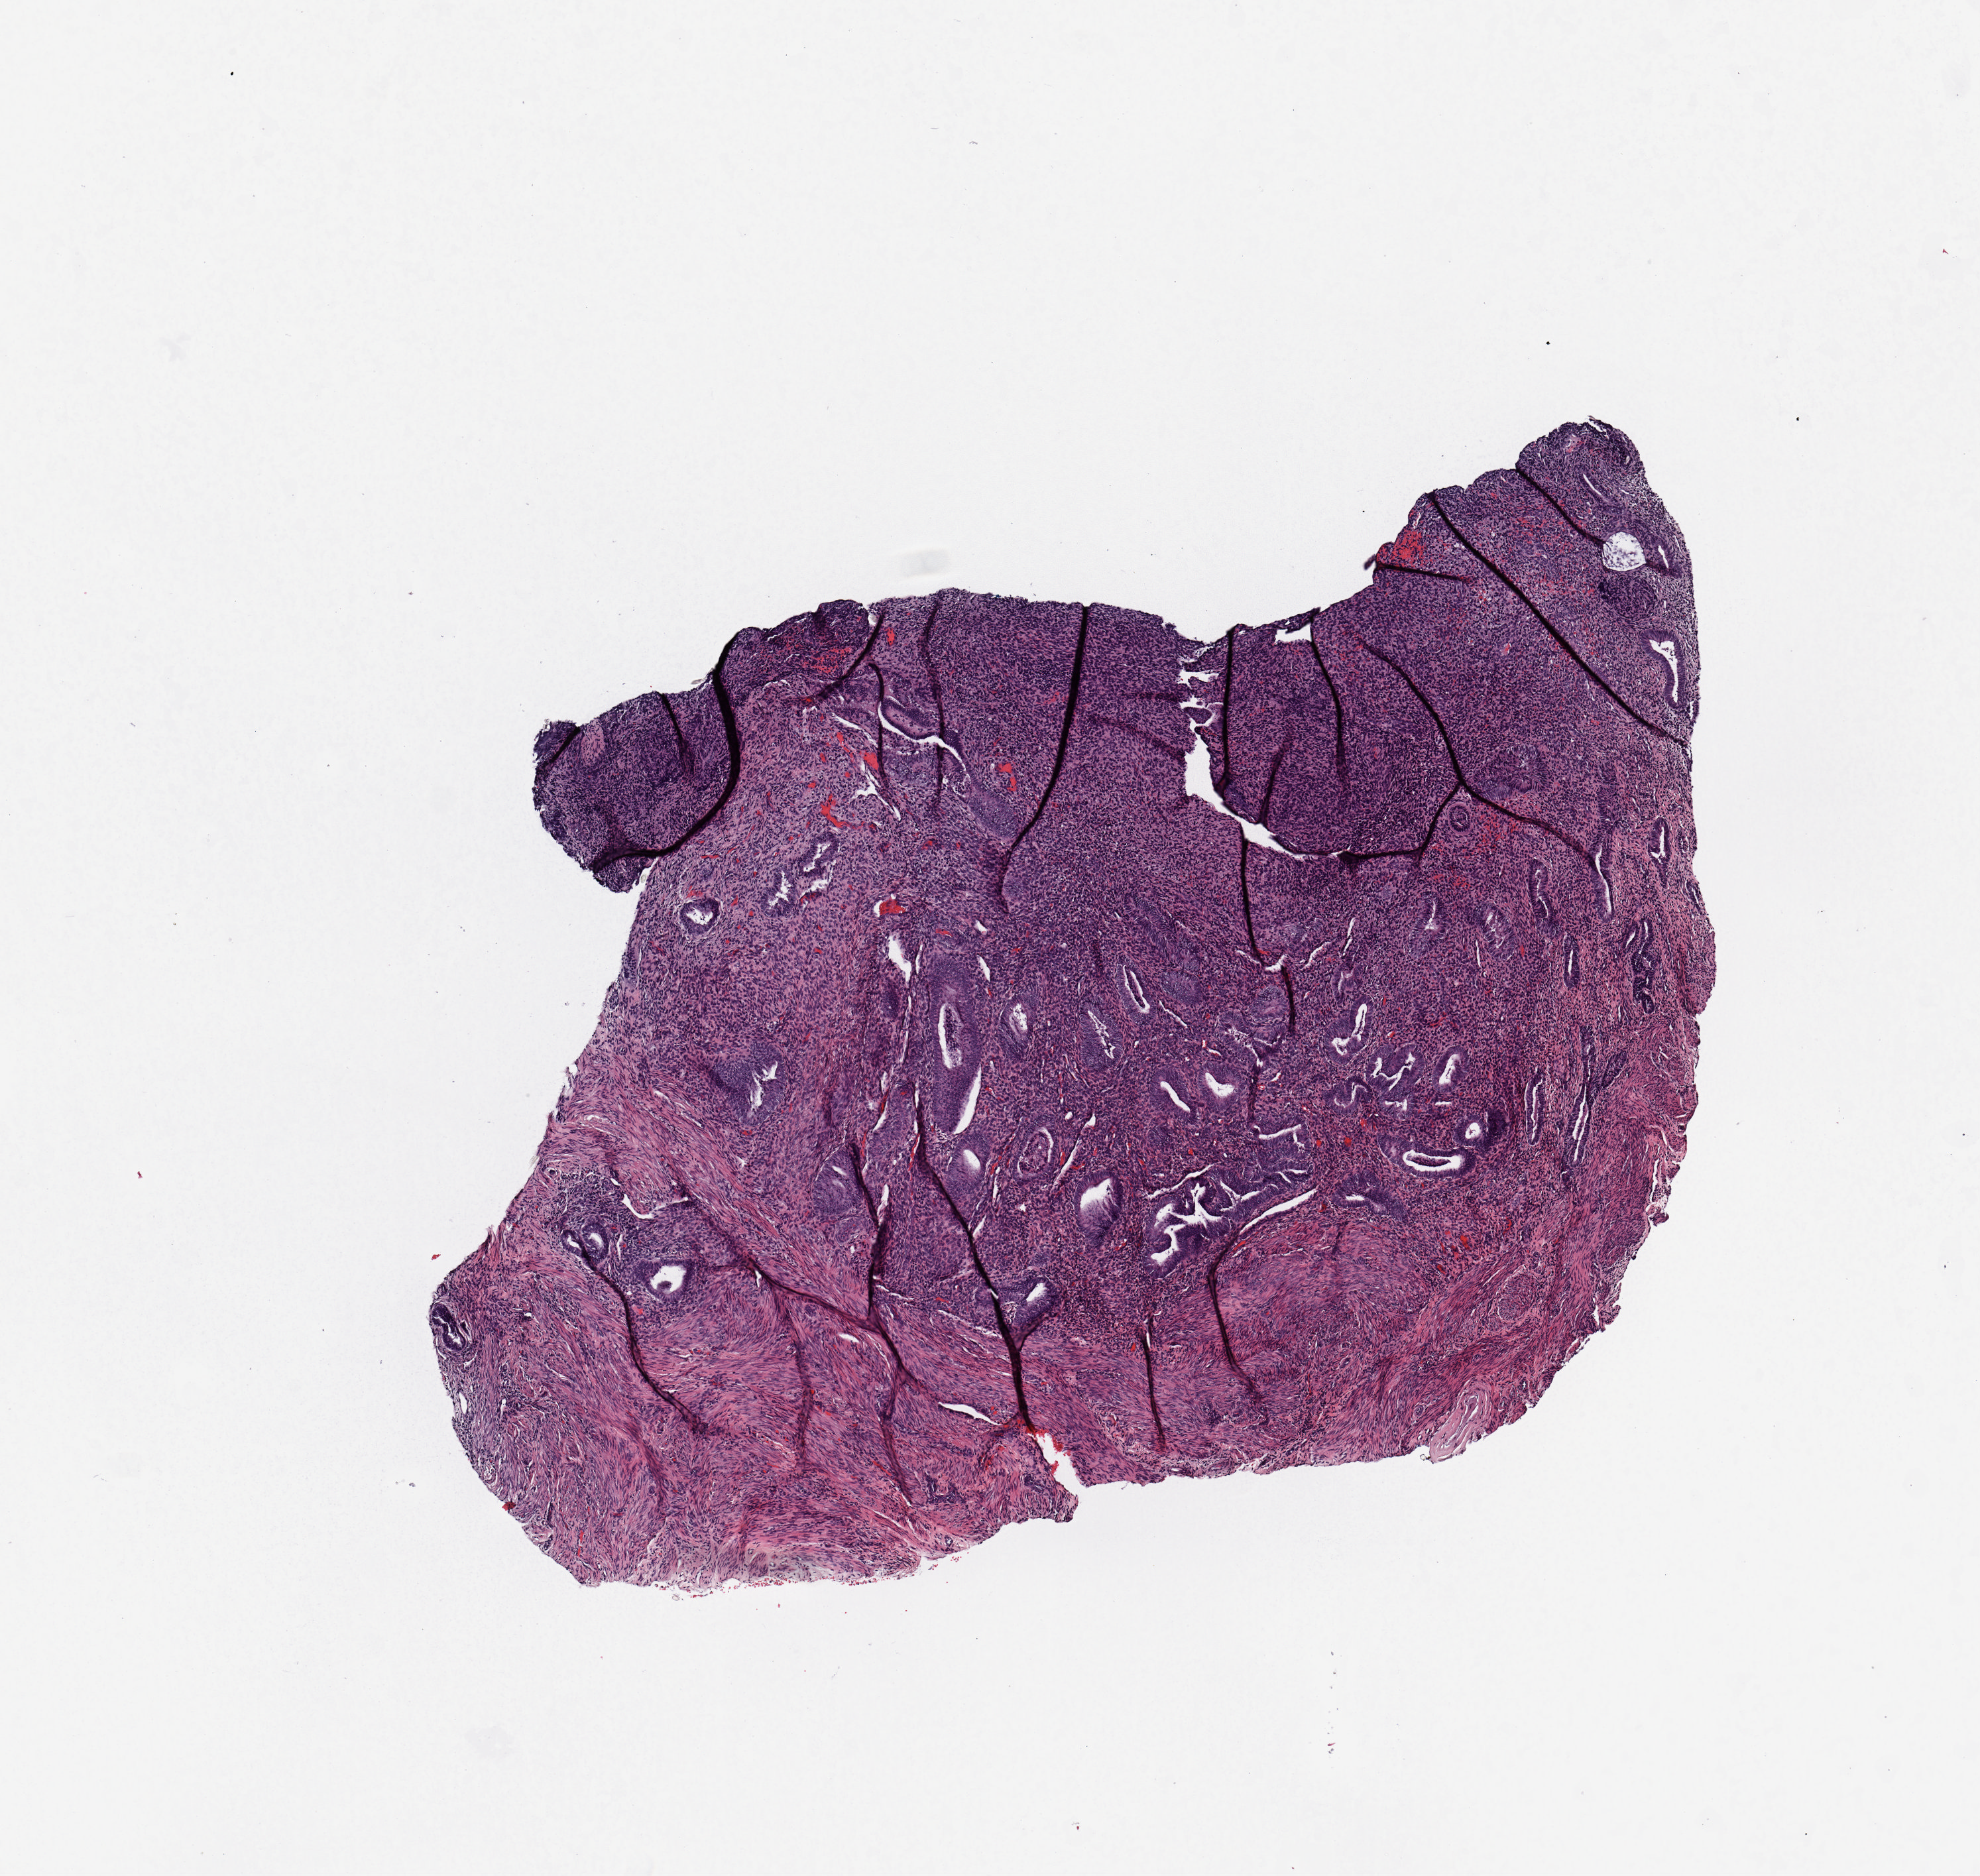
Hematoxylin and eosin (H&E) stained whole-slide image — a low-resolution overview of the entire scanned area, about 5.9 x 5.6 mm; uterus, normal (non-tumour) tissue. Patient: female, age 69 years.
• this section: normal (non-tumour) tissue from the same patient
• patient diagnosis: Endometrioid adenocarcinoma, NOS